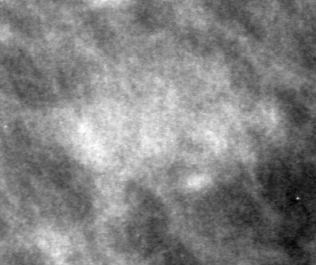
Region of interest cut from a scanned film mammogram (one marked finding), right breast, MLO view.
Finding: mass, shape oval, margins ill defined; BI-RADS assessment category 4; pathology (as recorded): benign.